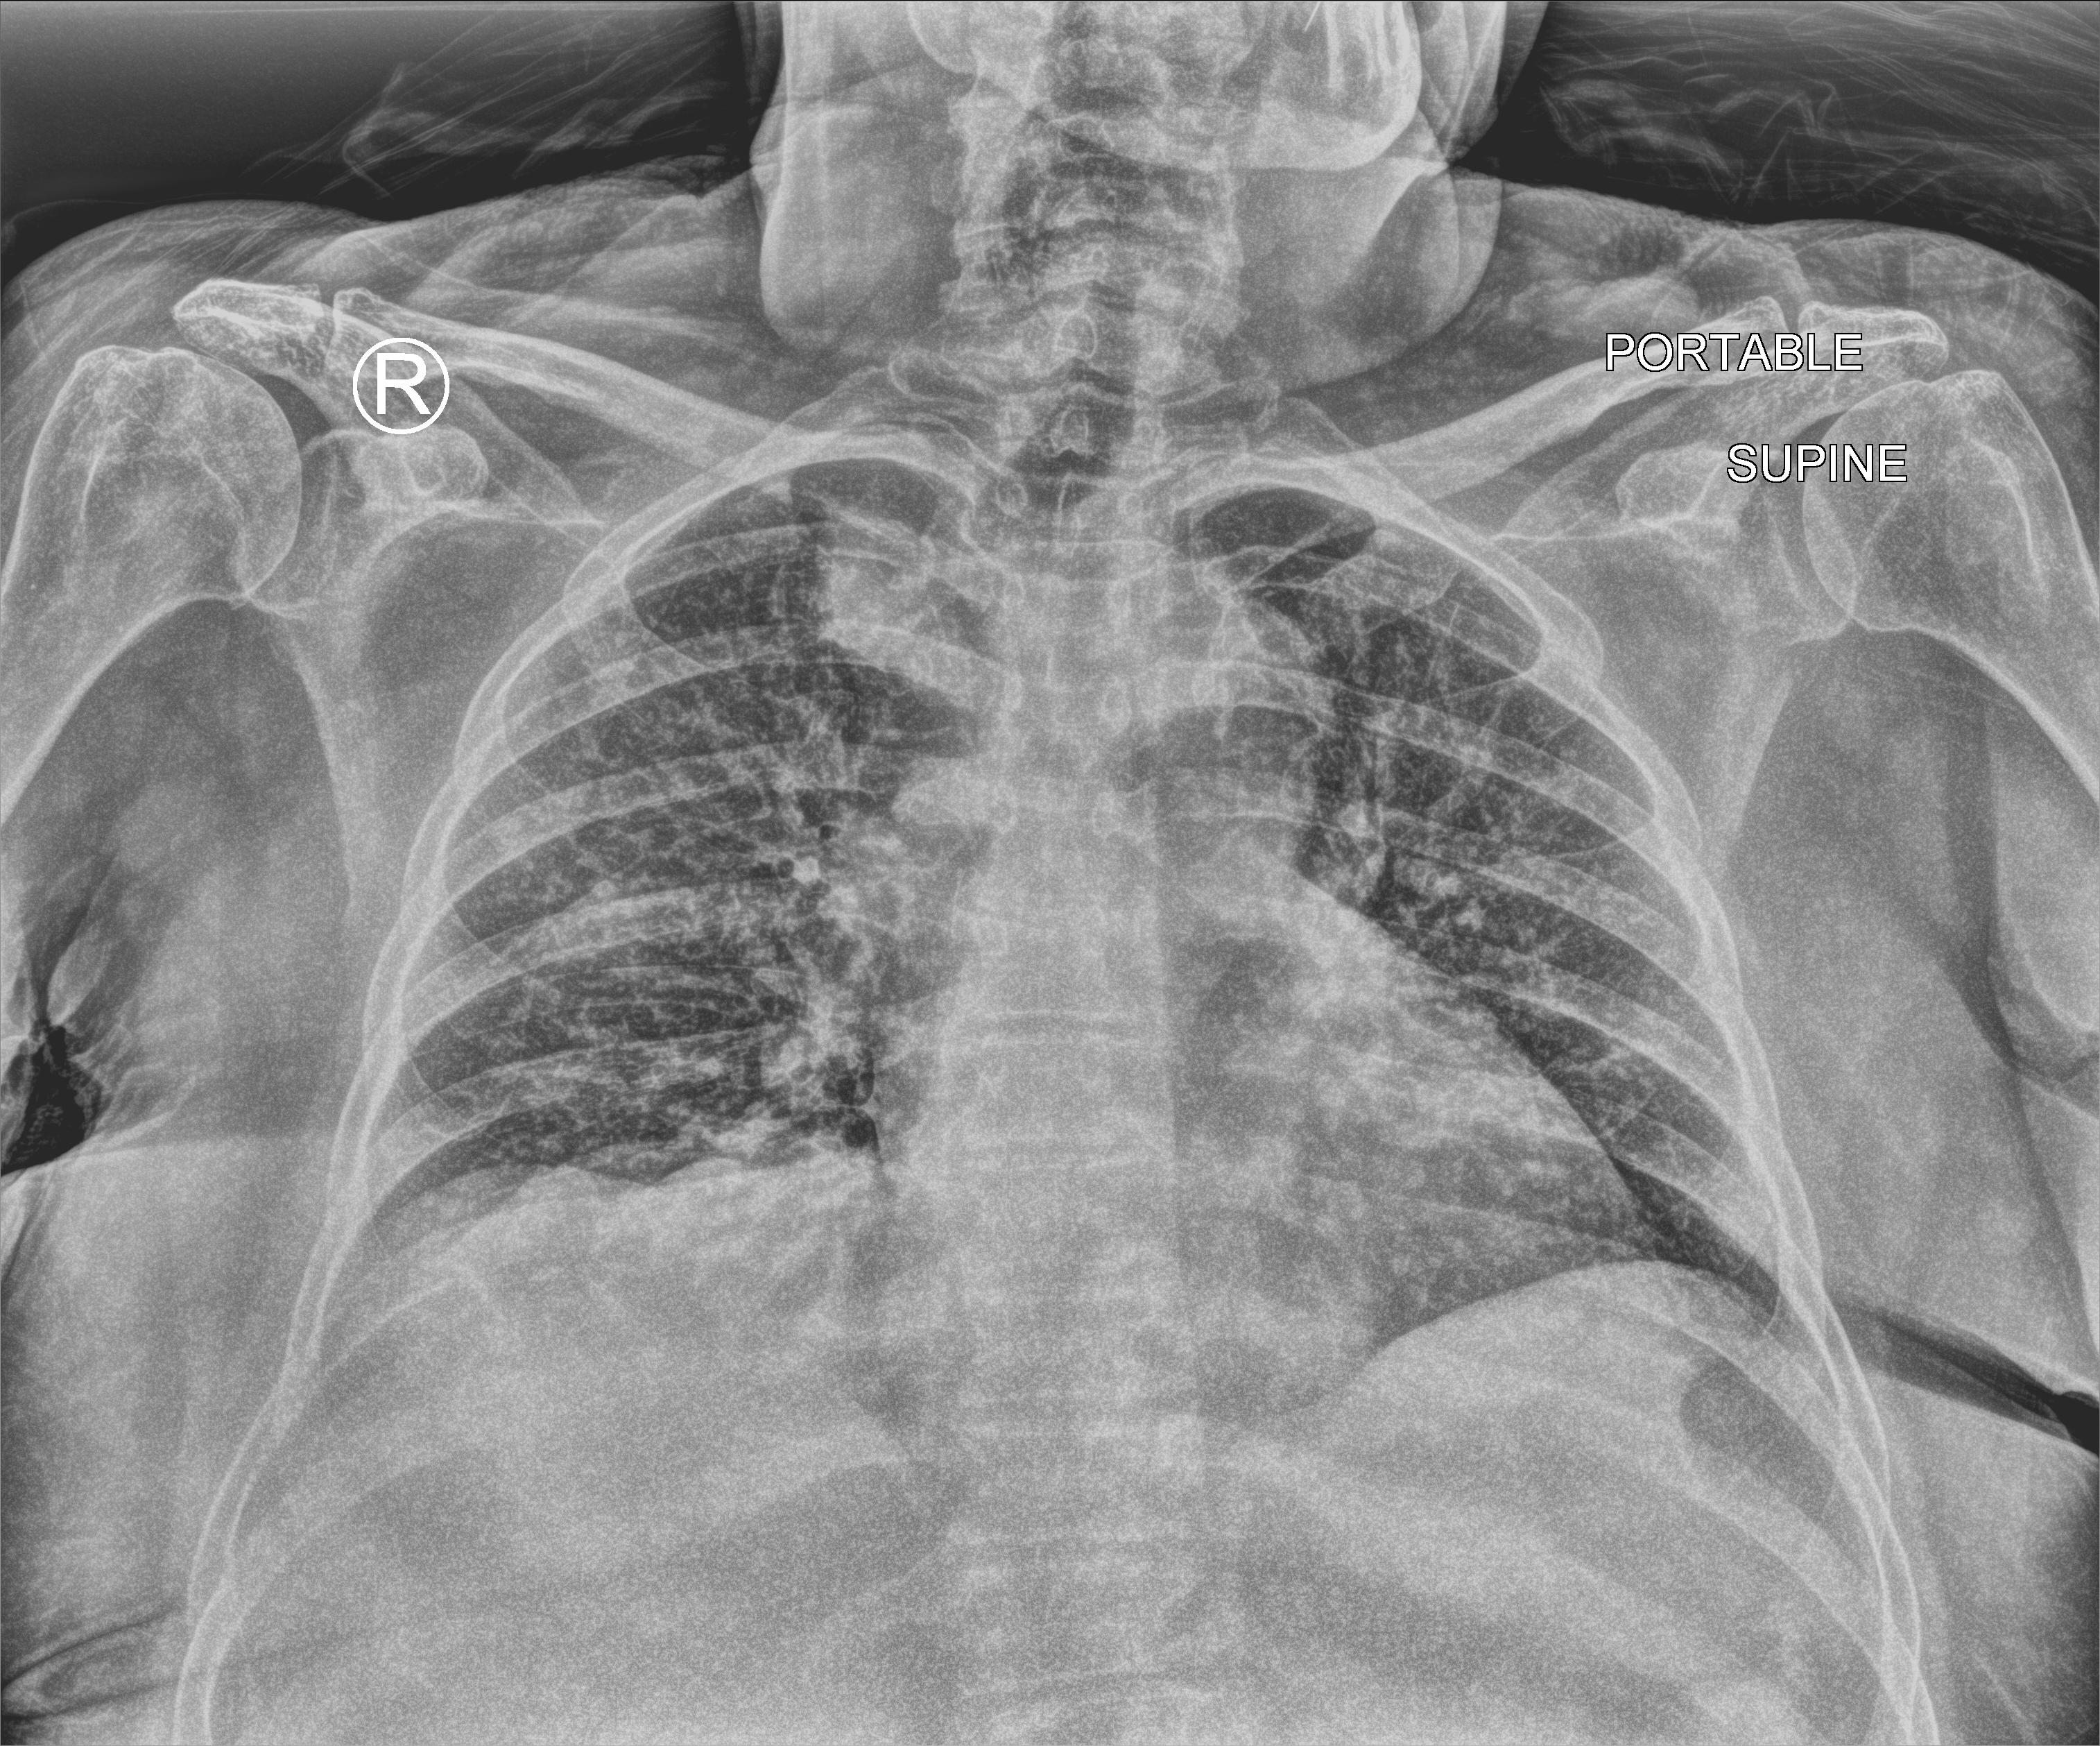
Portable chest radiograph; anteroposterior (AP) projection. Patient hospitalised with COVID-19; female, aged 75–90 years.
Hospital-stay facts (about this admission, not read from this image; timing relative to this image not recorded): mechanically ventilated during this hospital stay: no; length of hospital stay: 14 days.